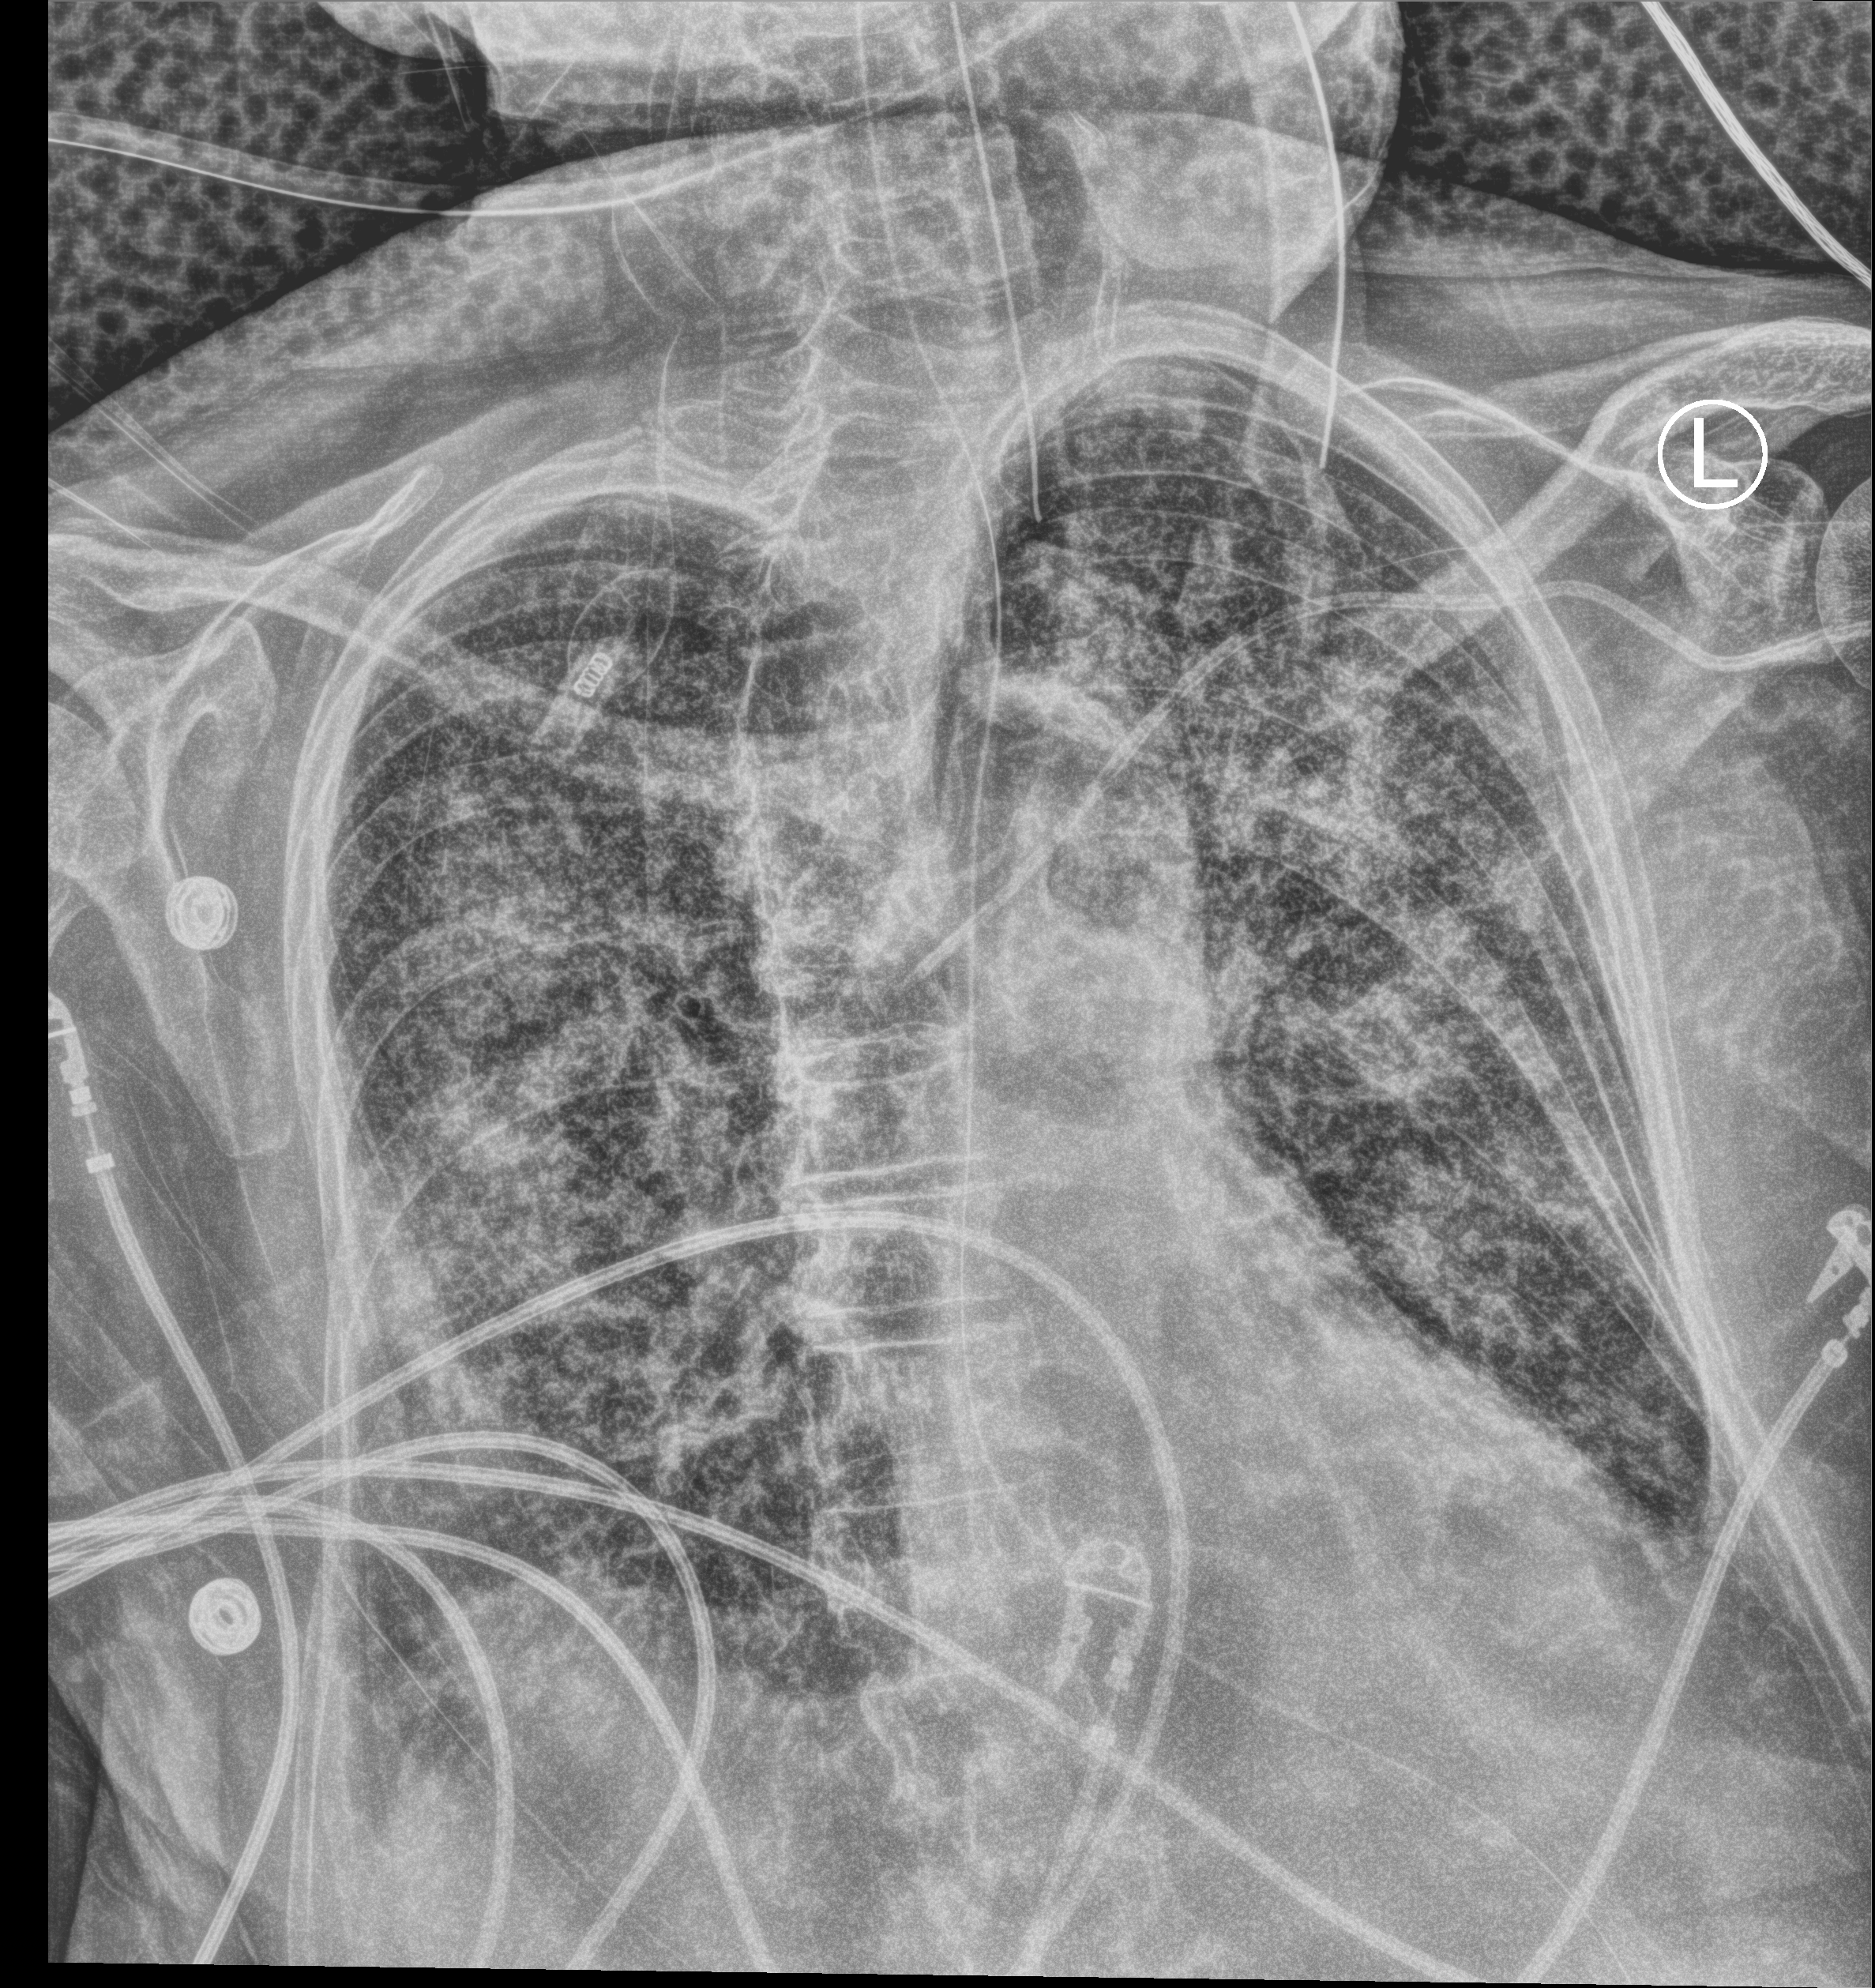
Chest X-ray (portable), anteroposterior (AP) projection. Female patient hospitalised with COVID-19, age 75–90 years.
From the hospital-stay record, not from the radiograph (when in the stay this image was taken is not recorded): length of hospital stay: 70 days; smoking status (admission record): former.